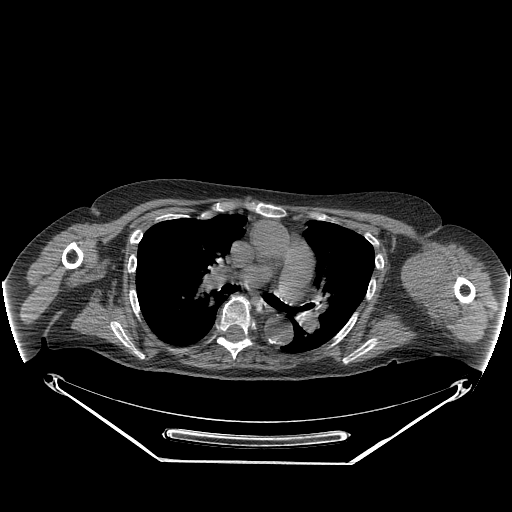
CT of an extremity soft-tissue mass (from a PET/CT study), one axial slice. Position 181 of 267 along the scan axis. Reconstruction kernel STANDARD. Soft-tissue window (W 400 / L 40 HU). 512 × 512 image matrix. Female patient. Case-level facts recorded for this patient, not image findings: histological type: pleiomorphic leiomyosarcoma; grade: high; site of the primary tumour: left biceps.
Outlined on this slice (expert contour drawn on MRI and transferred to this co-registered scan by the dataset authors):
- gross tumour volume including surrounding oedema: bounding box [x1, y1, x2, y2] px = [409, 251, 451, 312]
- gross tumour volume (mass): [409, 251, 451, 303]